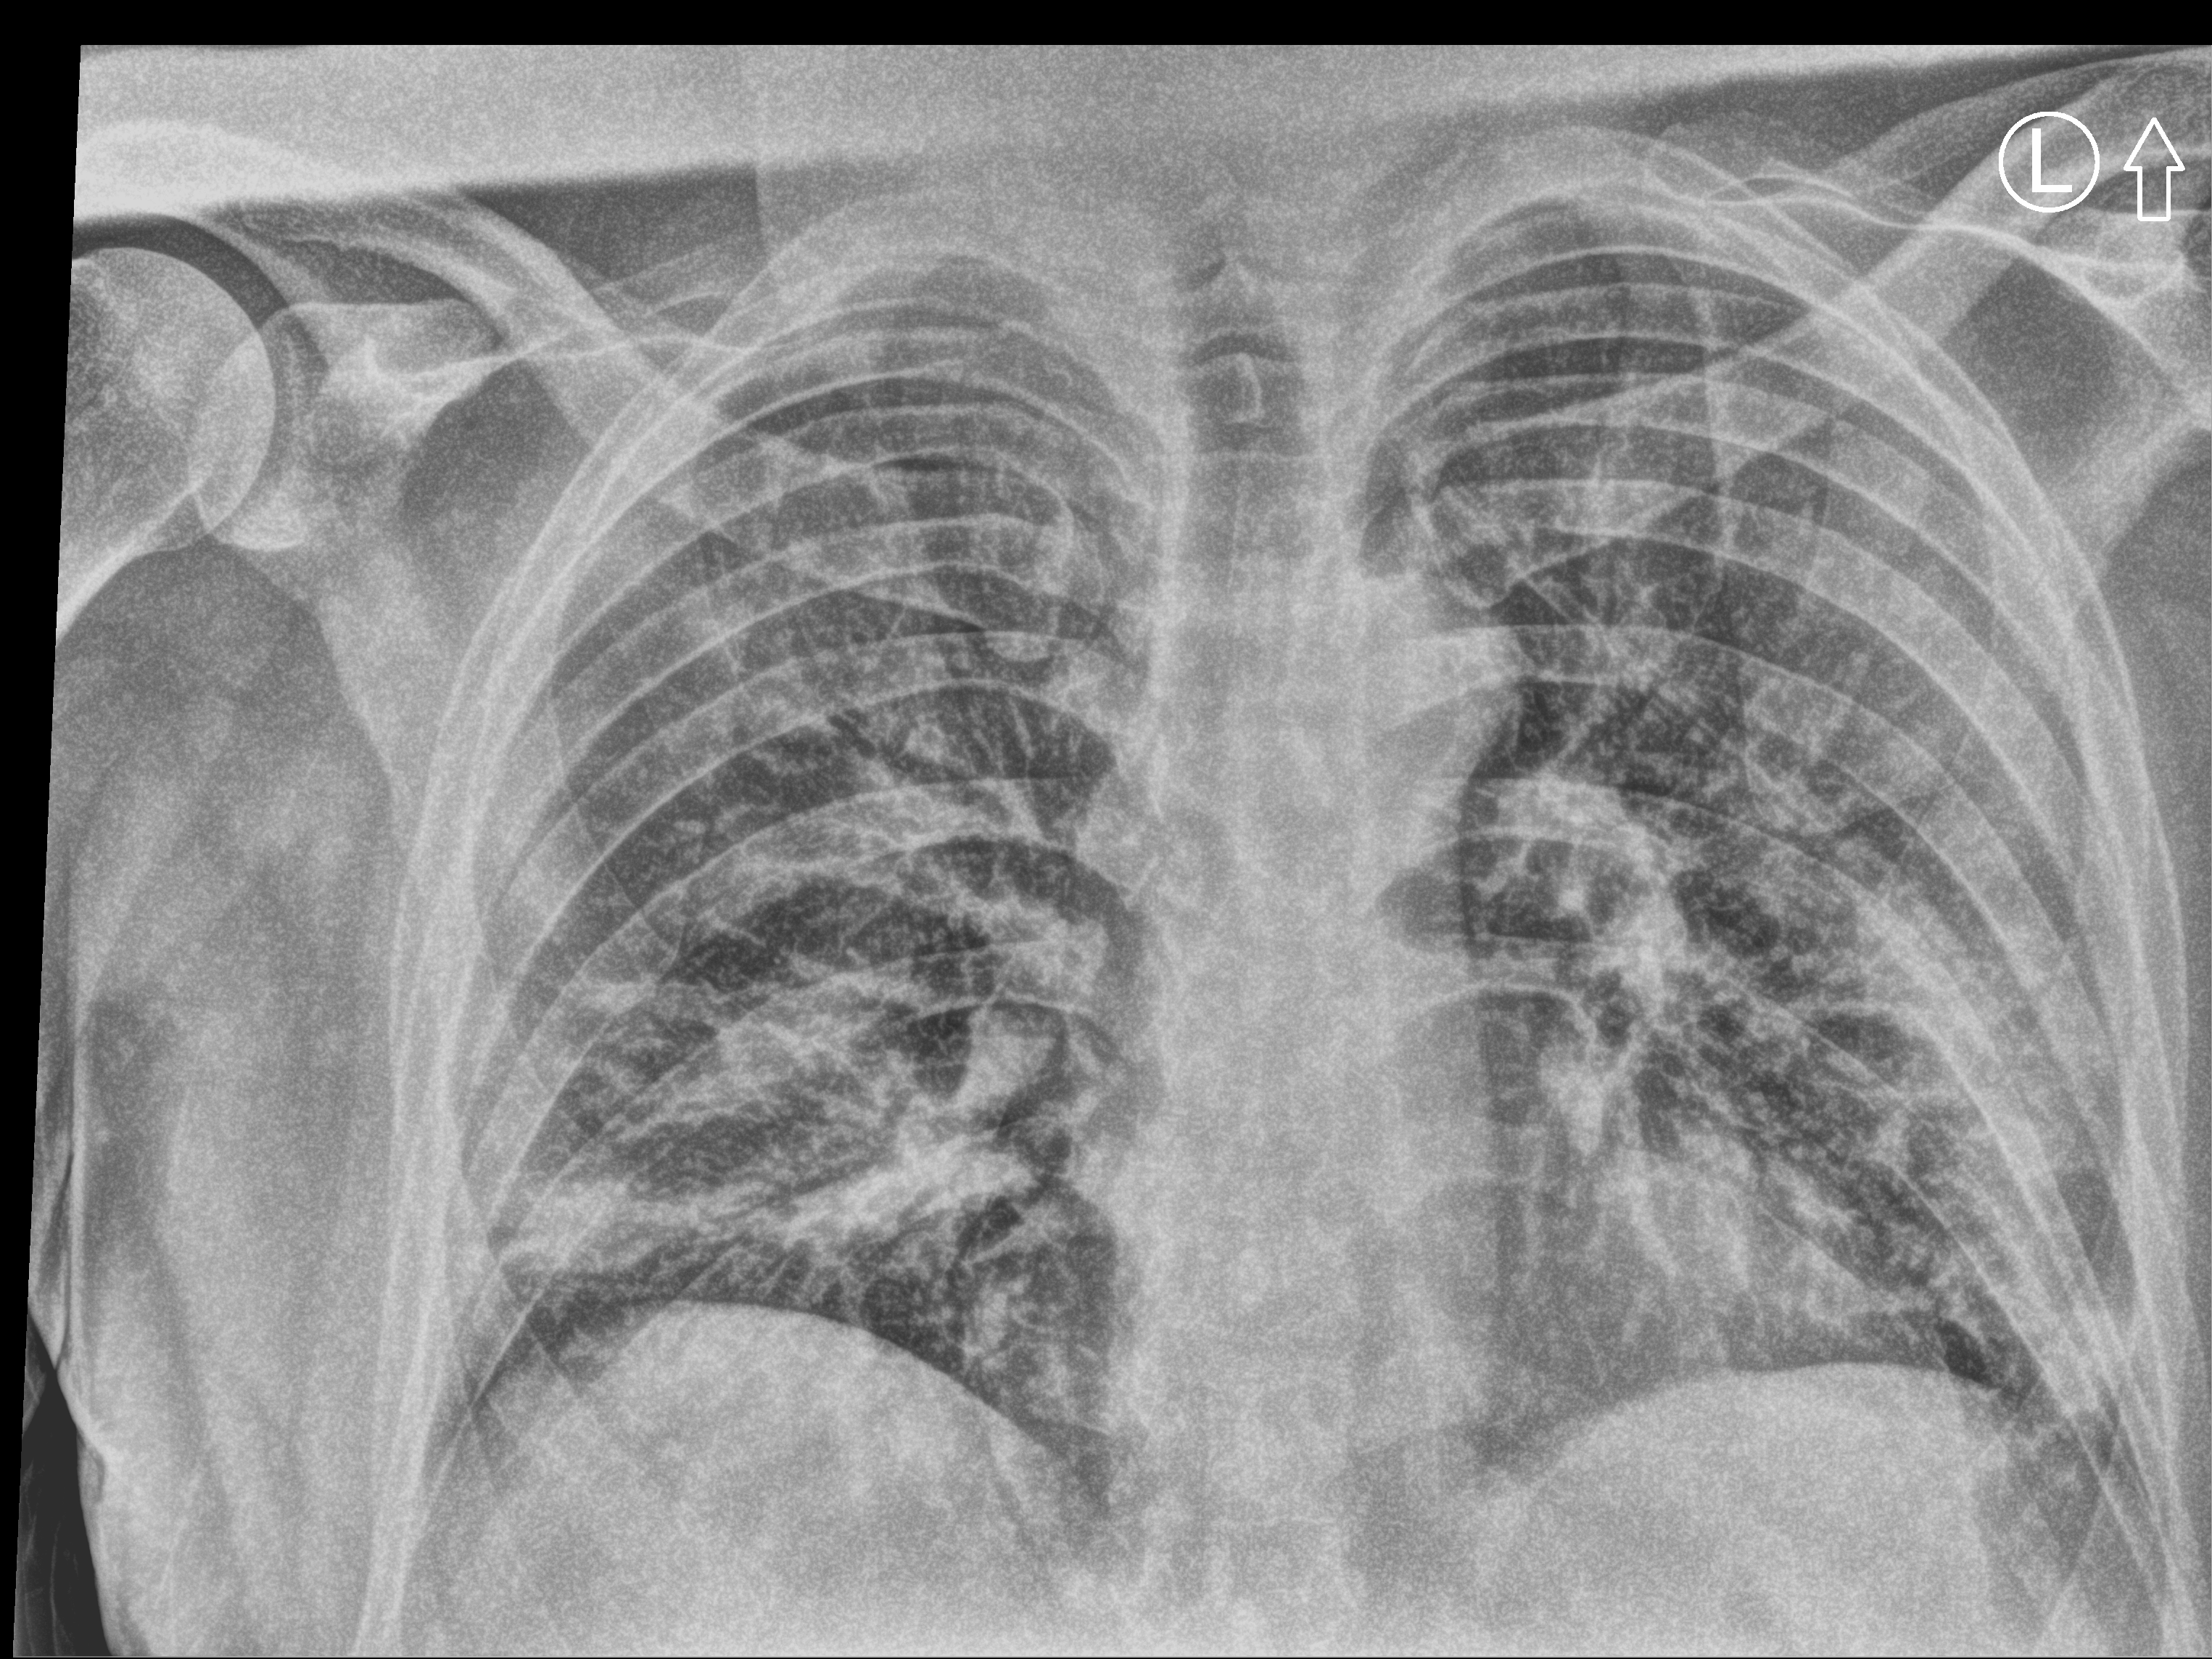
Bedside chest radiograph (computed radiography). Patient hospitalised with COVID-19; male, aged 18–59 years.
From the hospital-stay record, not from the radiograph (when in the stay this image was taken is not recorded): mechanically ventilated during this hospital stay: no; length of hospital stay: 10 days; diabetes (admission record): no.